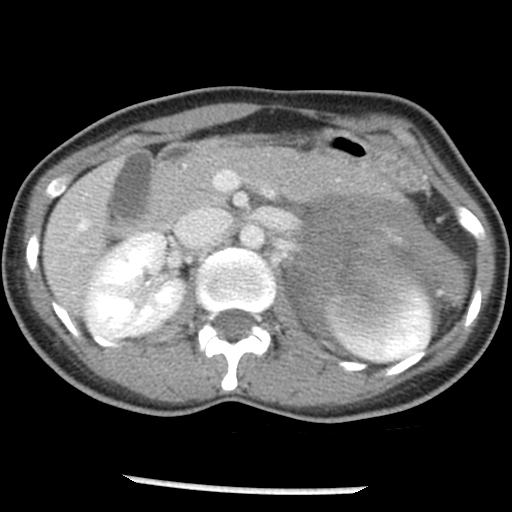
Contrast-enhanced abdominal CT, one axial slice. Position 25 of 54 along the scan axis. 120 kVp. Intravenous contrast given. Soft-tissue window (W 400 / L 40 HU). 512 × 512 image matrix, field of view 240 × 240 mm. Patient: female, 33 years. Case-level facts recorded for this patient, not image findings: diagnosis: adrenocortical carcinoma; tumour side: left adrenal; tumour size at pathology: 11 cm; Ki-67 index: 20 %; stage (as recorded): 2.
Outlined on this slice (semi-automatically segmented with operator editing):
- mass: bounding box <292,197,462,334> (left, top, right, bottom; pixels)